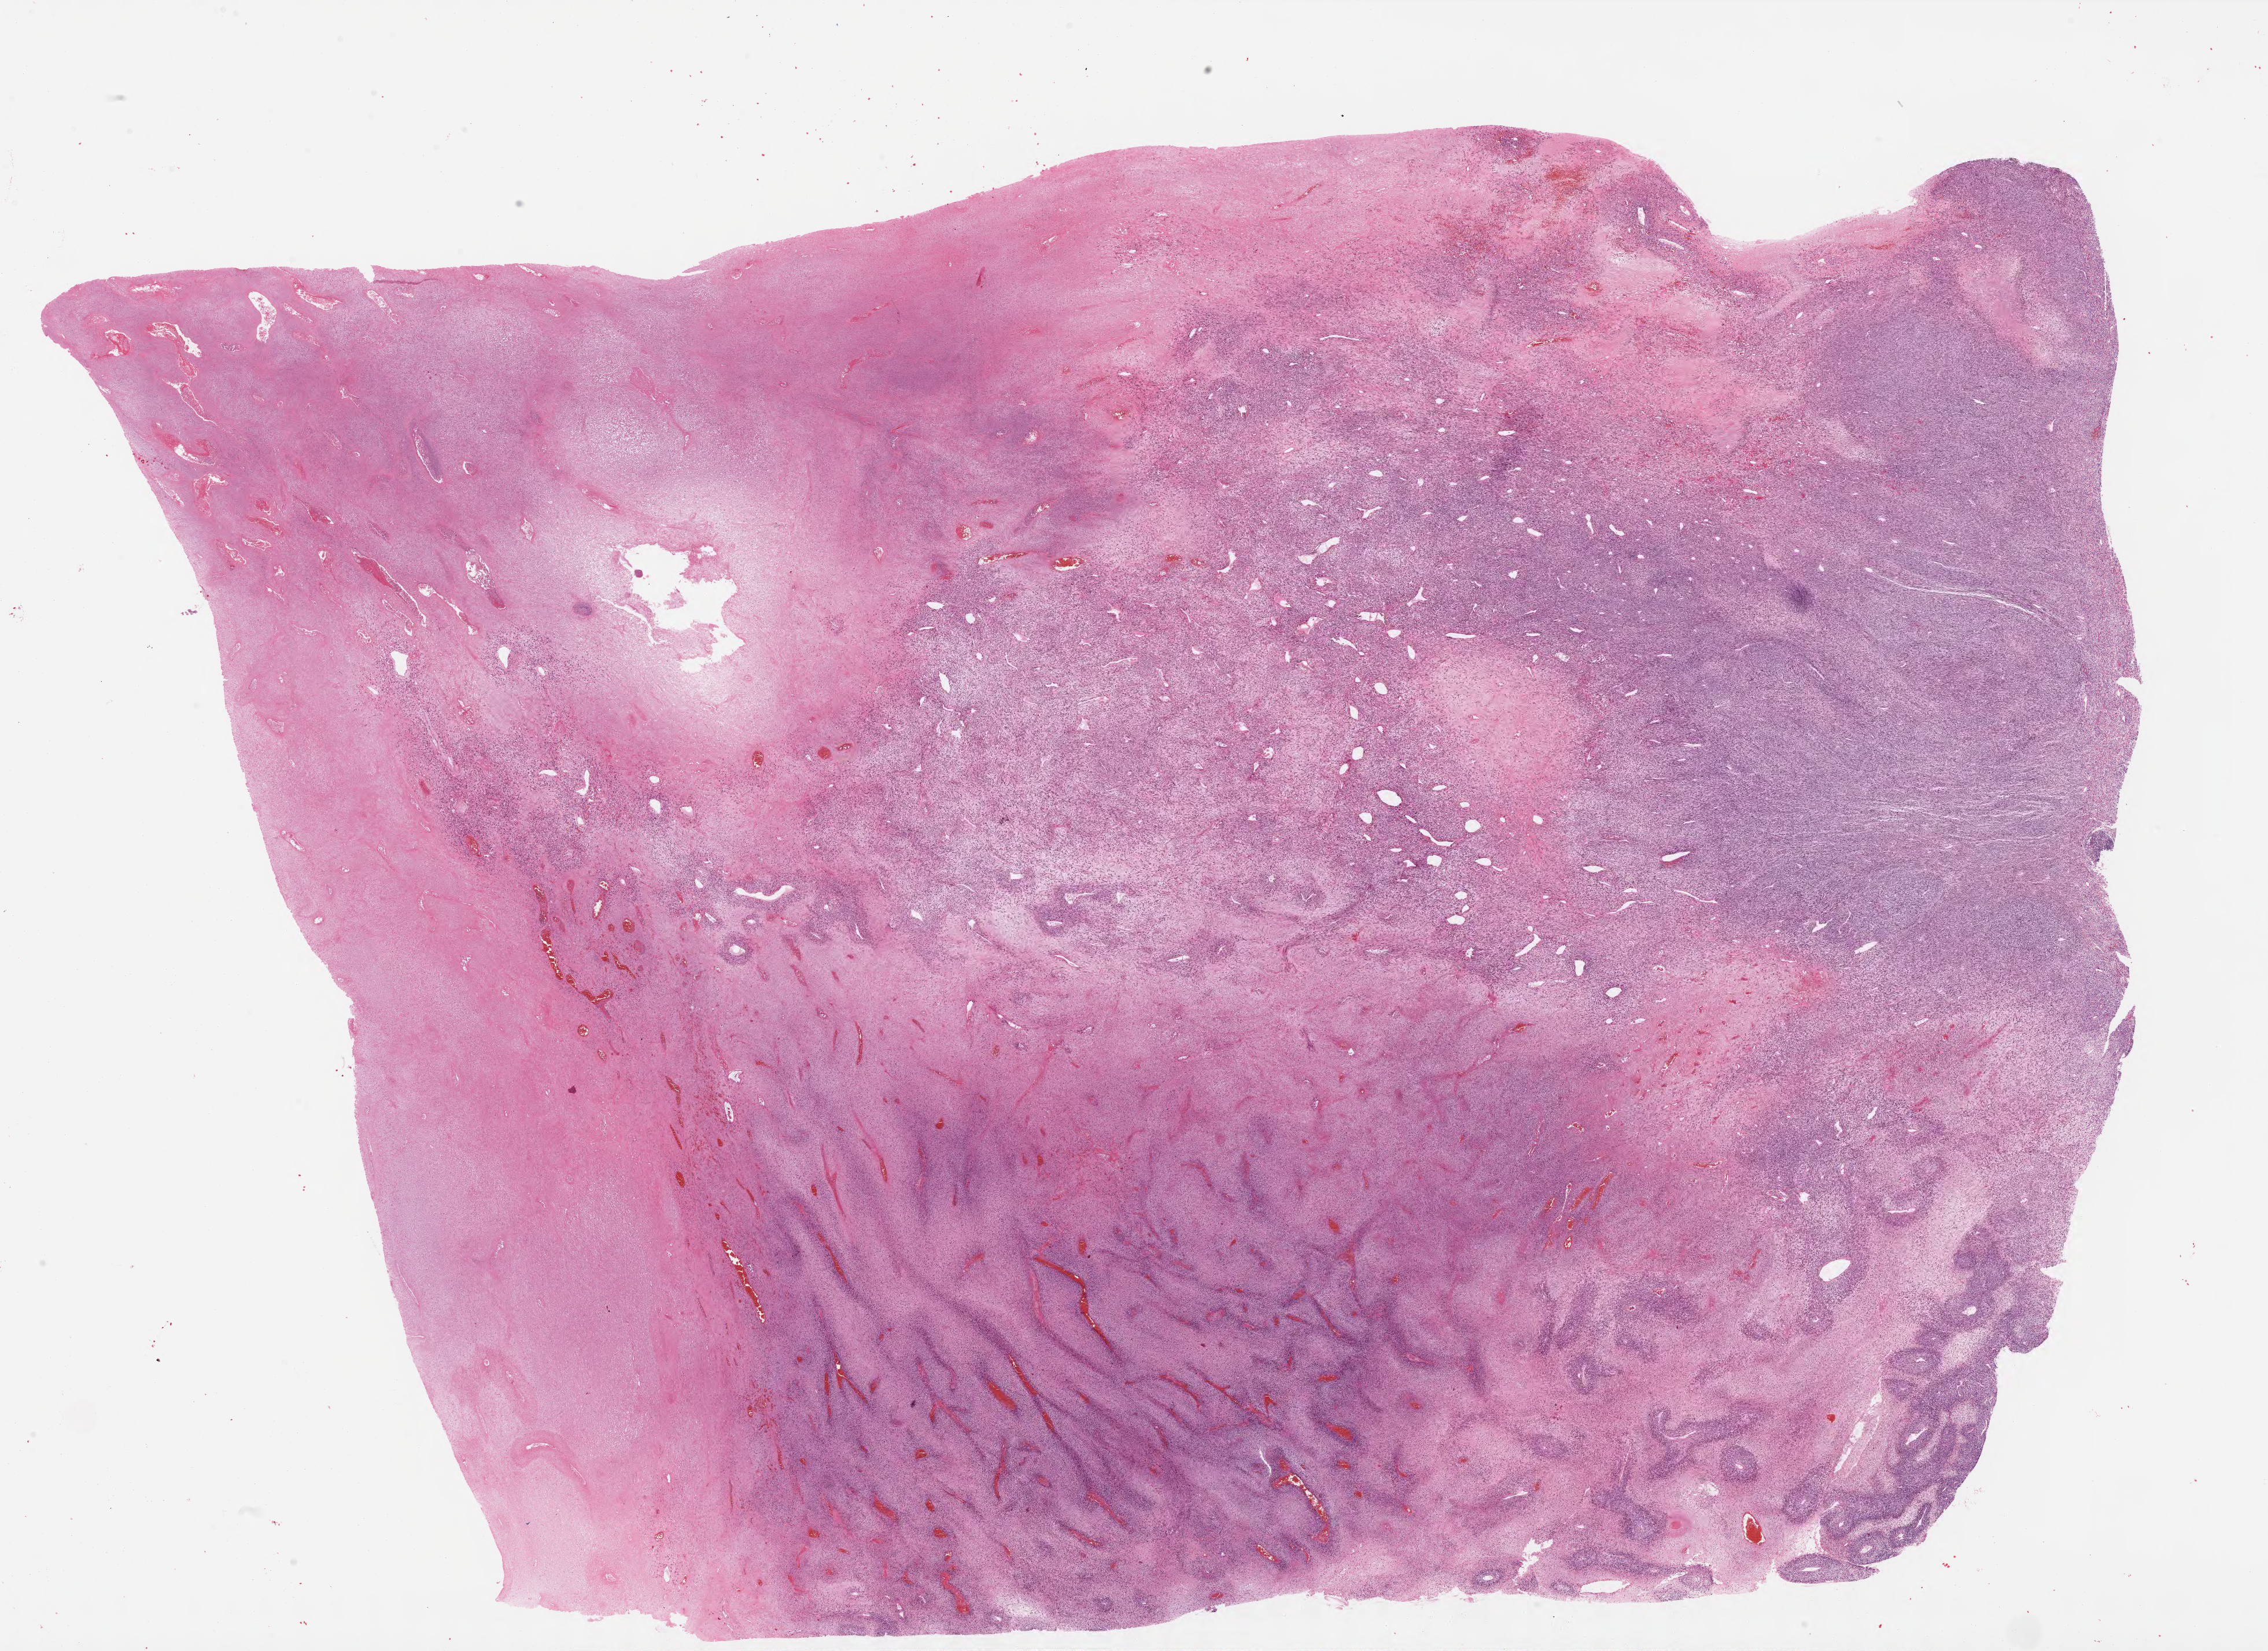
H&E whole-slide image, whole scanned area (about 30.9 x 22.5 mm, acquisition: 40x scan) shown as a low-resolution overview; formalin-fixed paraffin-embedded (FFPE) diagnostic section; sample: primary tumour, retroperitoneum and peritoneum. Female patient; age at initial diagnosis 44 years.
Histologic diagnosis: Dedifferentiated liposarcoma (retroperitoneum).